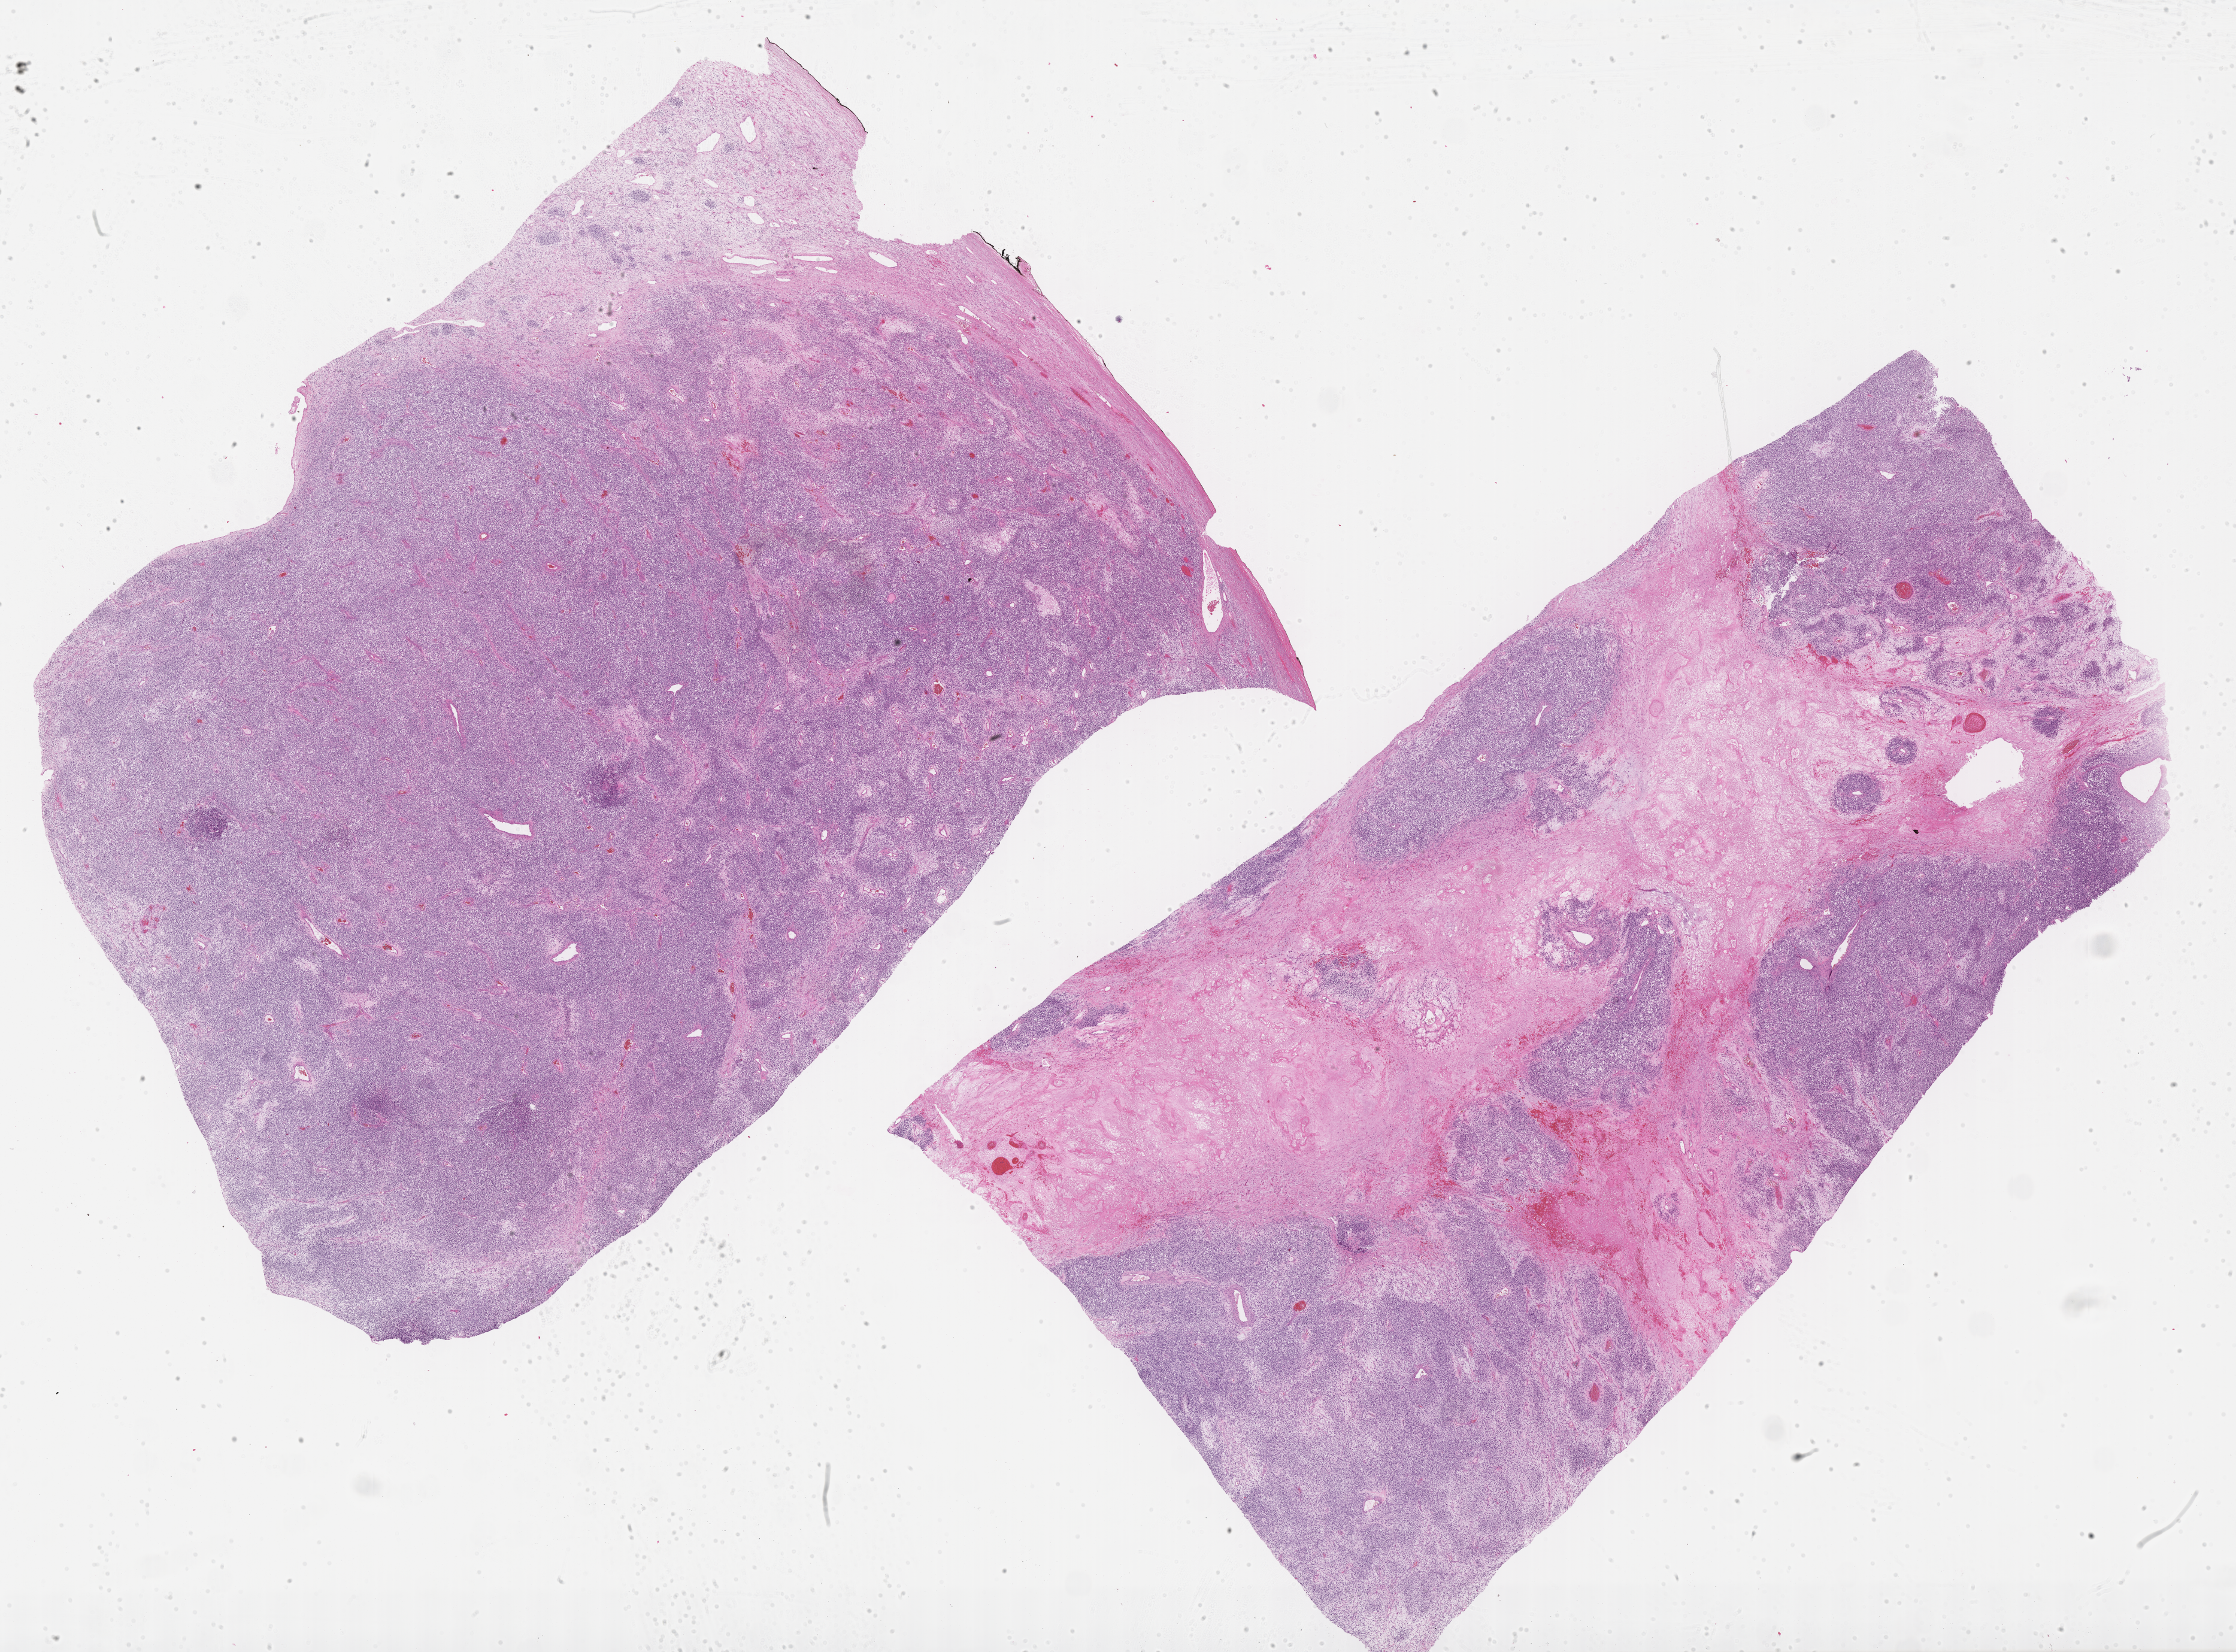
Digitized H&E-stained section of tumor tissue, a low-resolution overview of the entire scanned area, about 30.2 x 22.3 mm, formalin-fixed paraffin-embedded section, sample anatomic site: testicle, right. Patient: male, age 8.8 years at diagnosis.
Diagnosis: rhabdomyosarcoma; histological classification: embryonal rhabdomyosarcoma.